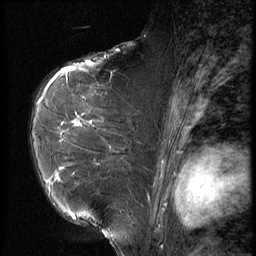
Breast MRI (dynamic contrast-enhanced), one sagittal slice. Position 41 of 56 along the scan axis. 3 images stored at this slice position (order not interpretable as contrast timing). 1.5 T. TE 4.2 ms, TR 9 ms. 256 × 256 image matrix. Patient: female, 61 years. Case-level facts recorded for this patient, not image findings: setting: breast cancer imaged before/during neoadjuvant chemotherapy; receptor status: HR-positive, HER2-negative.
Annotated regions visible in this slice (semi-automatic segmentation, software-assisted and operator-edited):
- analysis volume of interest (the breast-tissue region the enhancement analysis was run in; not a lesion): bounding box (x1, y1, x2, y2) in pixels: (47, 89, 153, 191)
- tumour enhancement mask (voxels above the 140 % enhancement threshold inside the analysis volume of interest): (50, 121, 82, 182)